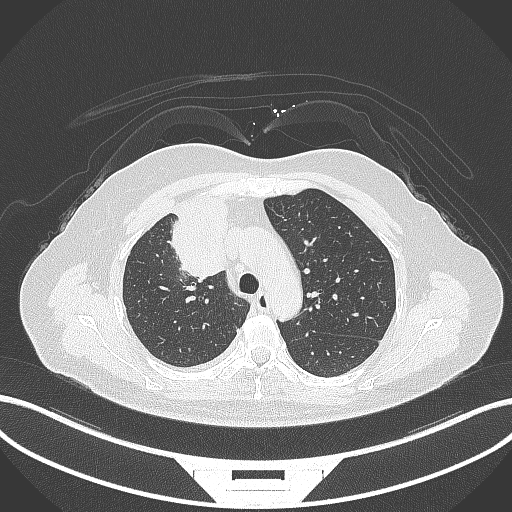
Chest CT, one axial slice. Reconstruction kernel B70f. 120 kVp. Lung window (W 1500 / L -600 HU). 1 mm slice thickness. 512 × 512 image matrix. Patient: female, 52 years. Case-level facts recorded for this patient, not image findings: clinical TNM (as recorded): T3 N1 M1.
Structures marked on this image (rectangle marked by the reading radiologist):
- lung tumour (recorded histology: adenocarcinoma): bounding box (x1, y1, x2, y2) in pixels: (164, 200, 235, 283)